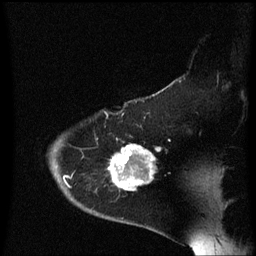
Breast MRI (dynamic contrast-enhanced), one sagittal slice; position 48 of 60 along the scan axis; dynamic contrast-enhanced series, image 2 of 3 at this slice position (ordered by acquisition); 1.5 T; TE 4.2 ms, TR 8.4 ms; 256 × 256 image matrix. Patient: female, 54 years. From the clinical record (not read from this slice): setting: breast cancer imaged before/during neoadjuvant chemotherapy; receptor status: HR-positive, HER2-negative.
Annotated regions visible in this slice (semi-automatic segmentation, software-assisted and operator-edited):
- analysis volume of interest (the breast-tissue region the enhancement analysis was run in; not a lesion): box from (x=110, y=136) to (x=163, y=199) px
- tumour enhancement mask (voxels above the 70 % enhancement threshold inside the analysis volume of interest): (x=111, y=144)–(x=156, y=191)